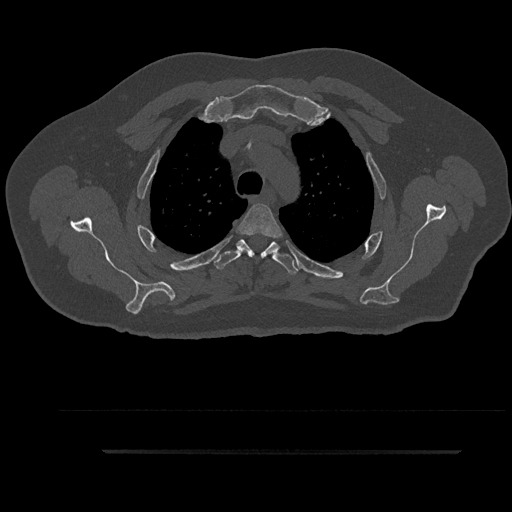
CT including the spine, one axial slice. 120 kVp. Bone window (W 1800 / L 400 HU). 512 × 512 image matrix. Male patient, age 63 years. From the clinical record (not read from this slice): primary cancer: renal.
Annotated regions visible in this slice (semi-automatic segmentation, software-assisted and operator-edited):
- T3 vertebra: bounding box (x1, y1, x2, y2) in pixels: (237, 204, 282, 238)
- T4 vertebra: (211, 239, 299, 274)